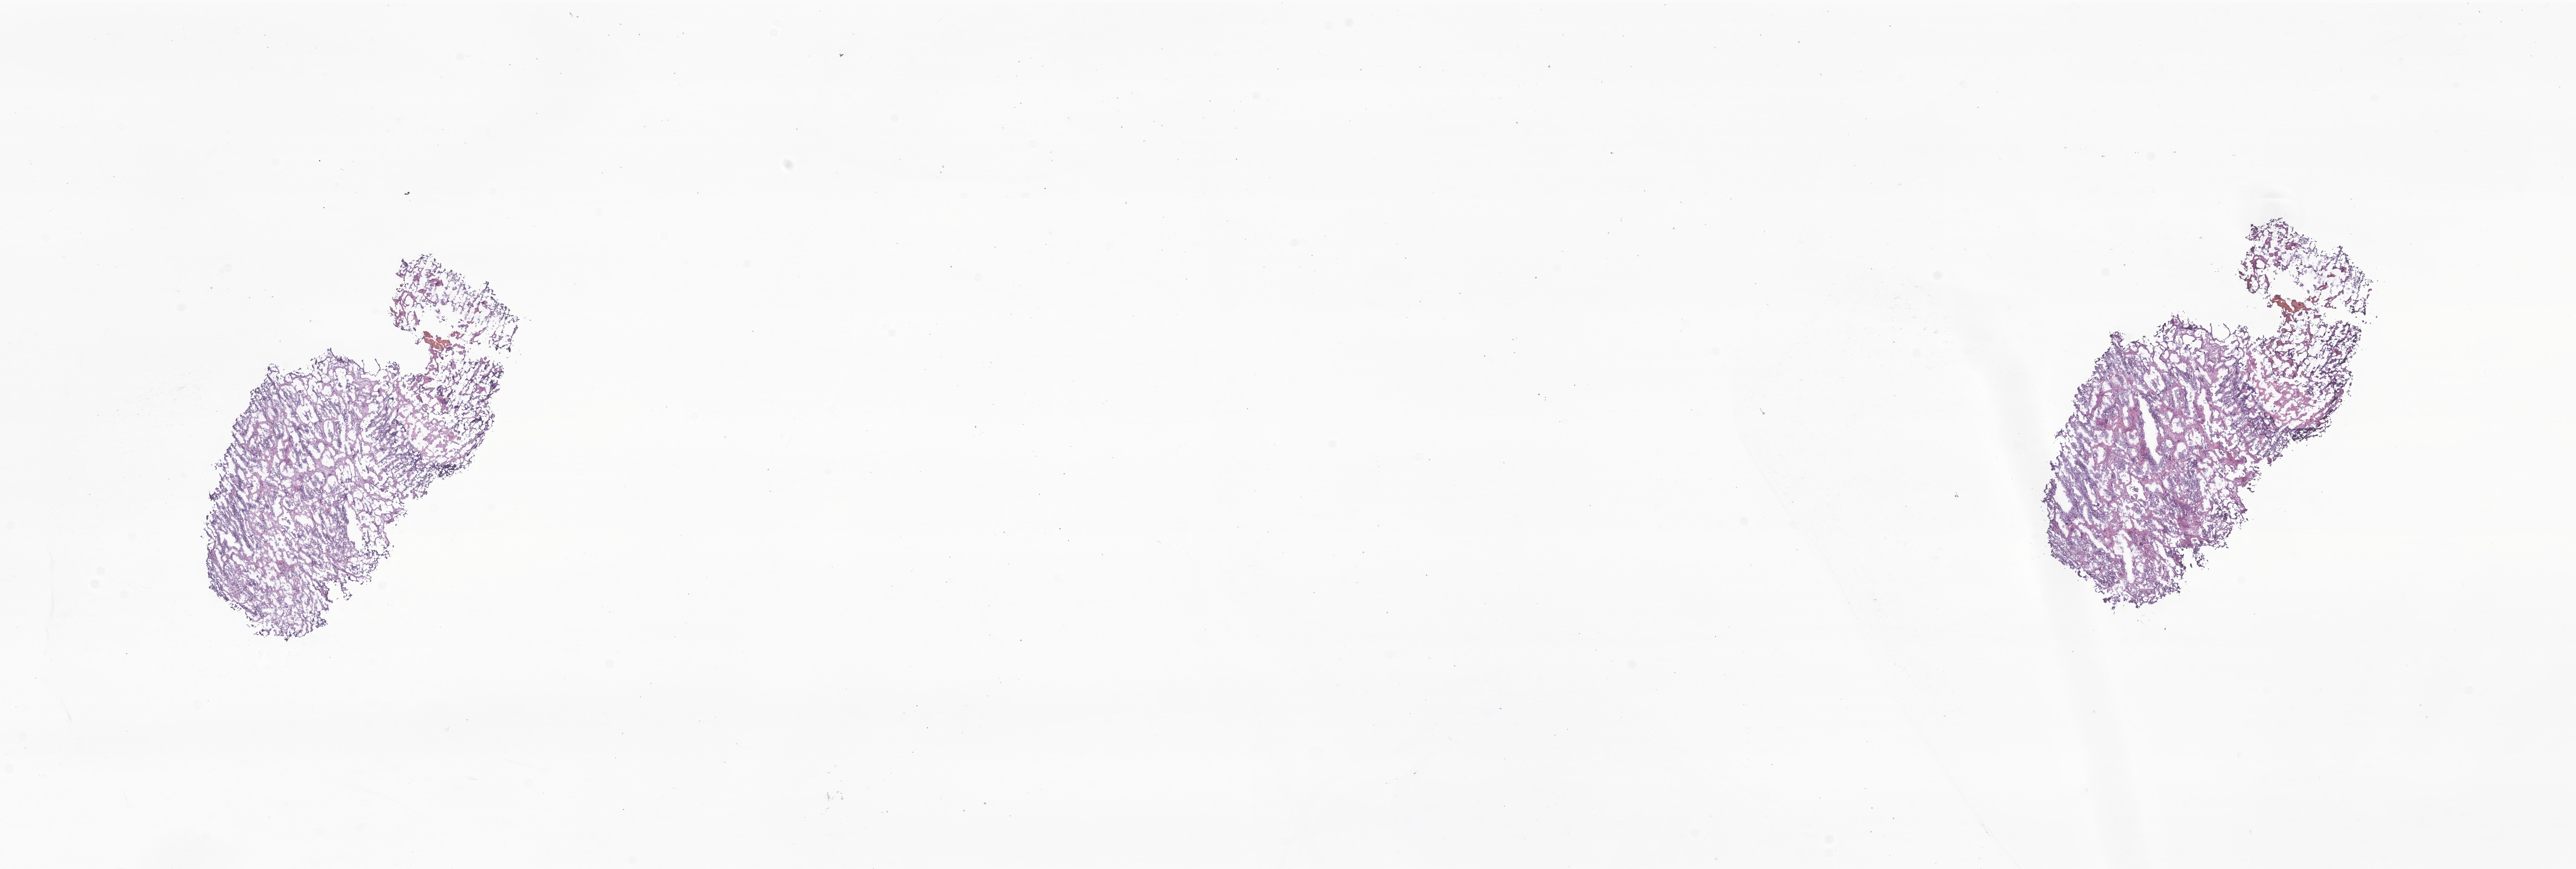
Whole-slide image, hematoxylin and eosin (H&E) stain of tumor tissue from the brain — shown as a low-resolution overview of the whole scanned area (about 24.5 x 8.3 mm); cryosection (OCT / tissue freezing medium). Patient: male, age 90 months (7 years 6 months).
* recorded diagnosis: Medulloblastoma, NOS